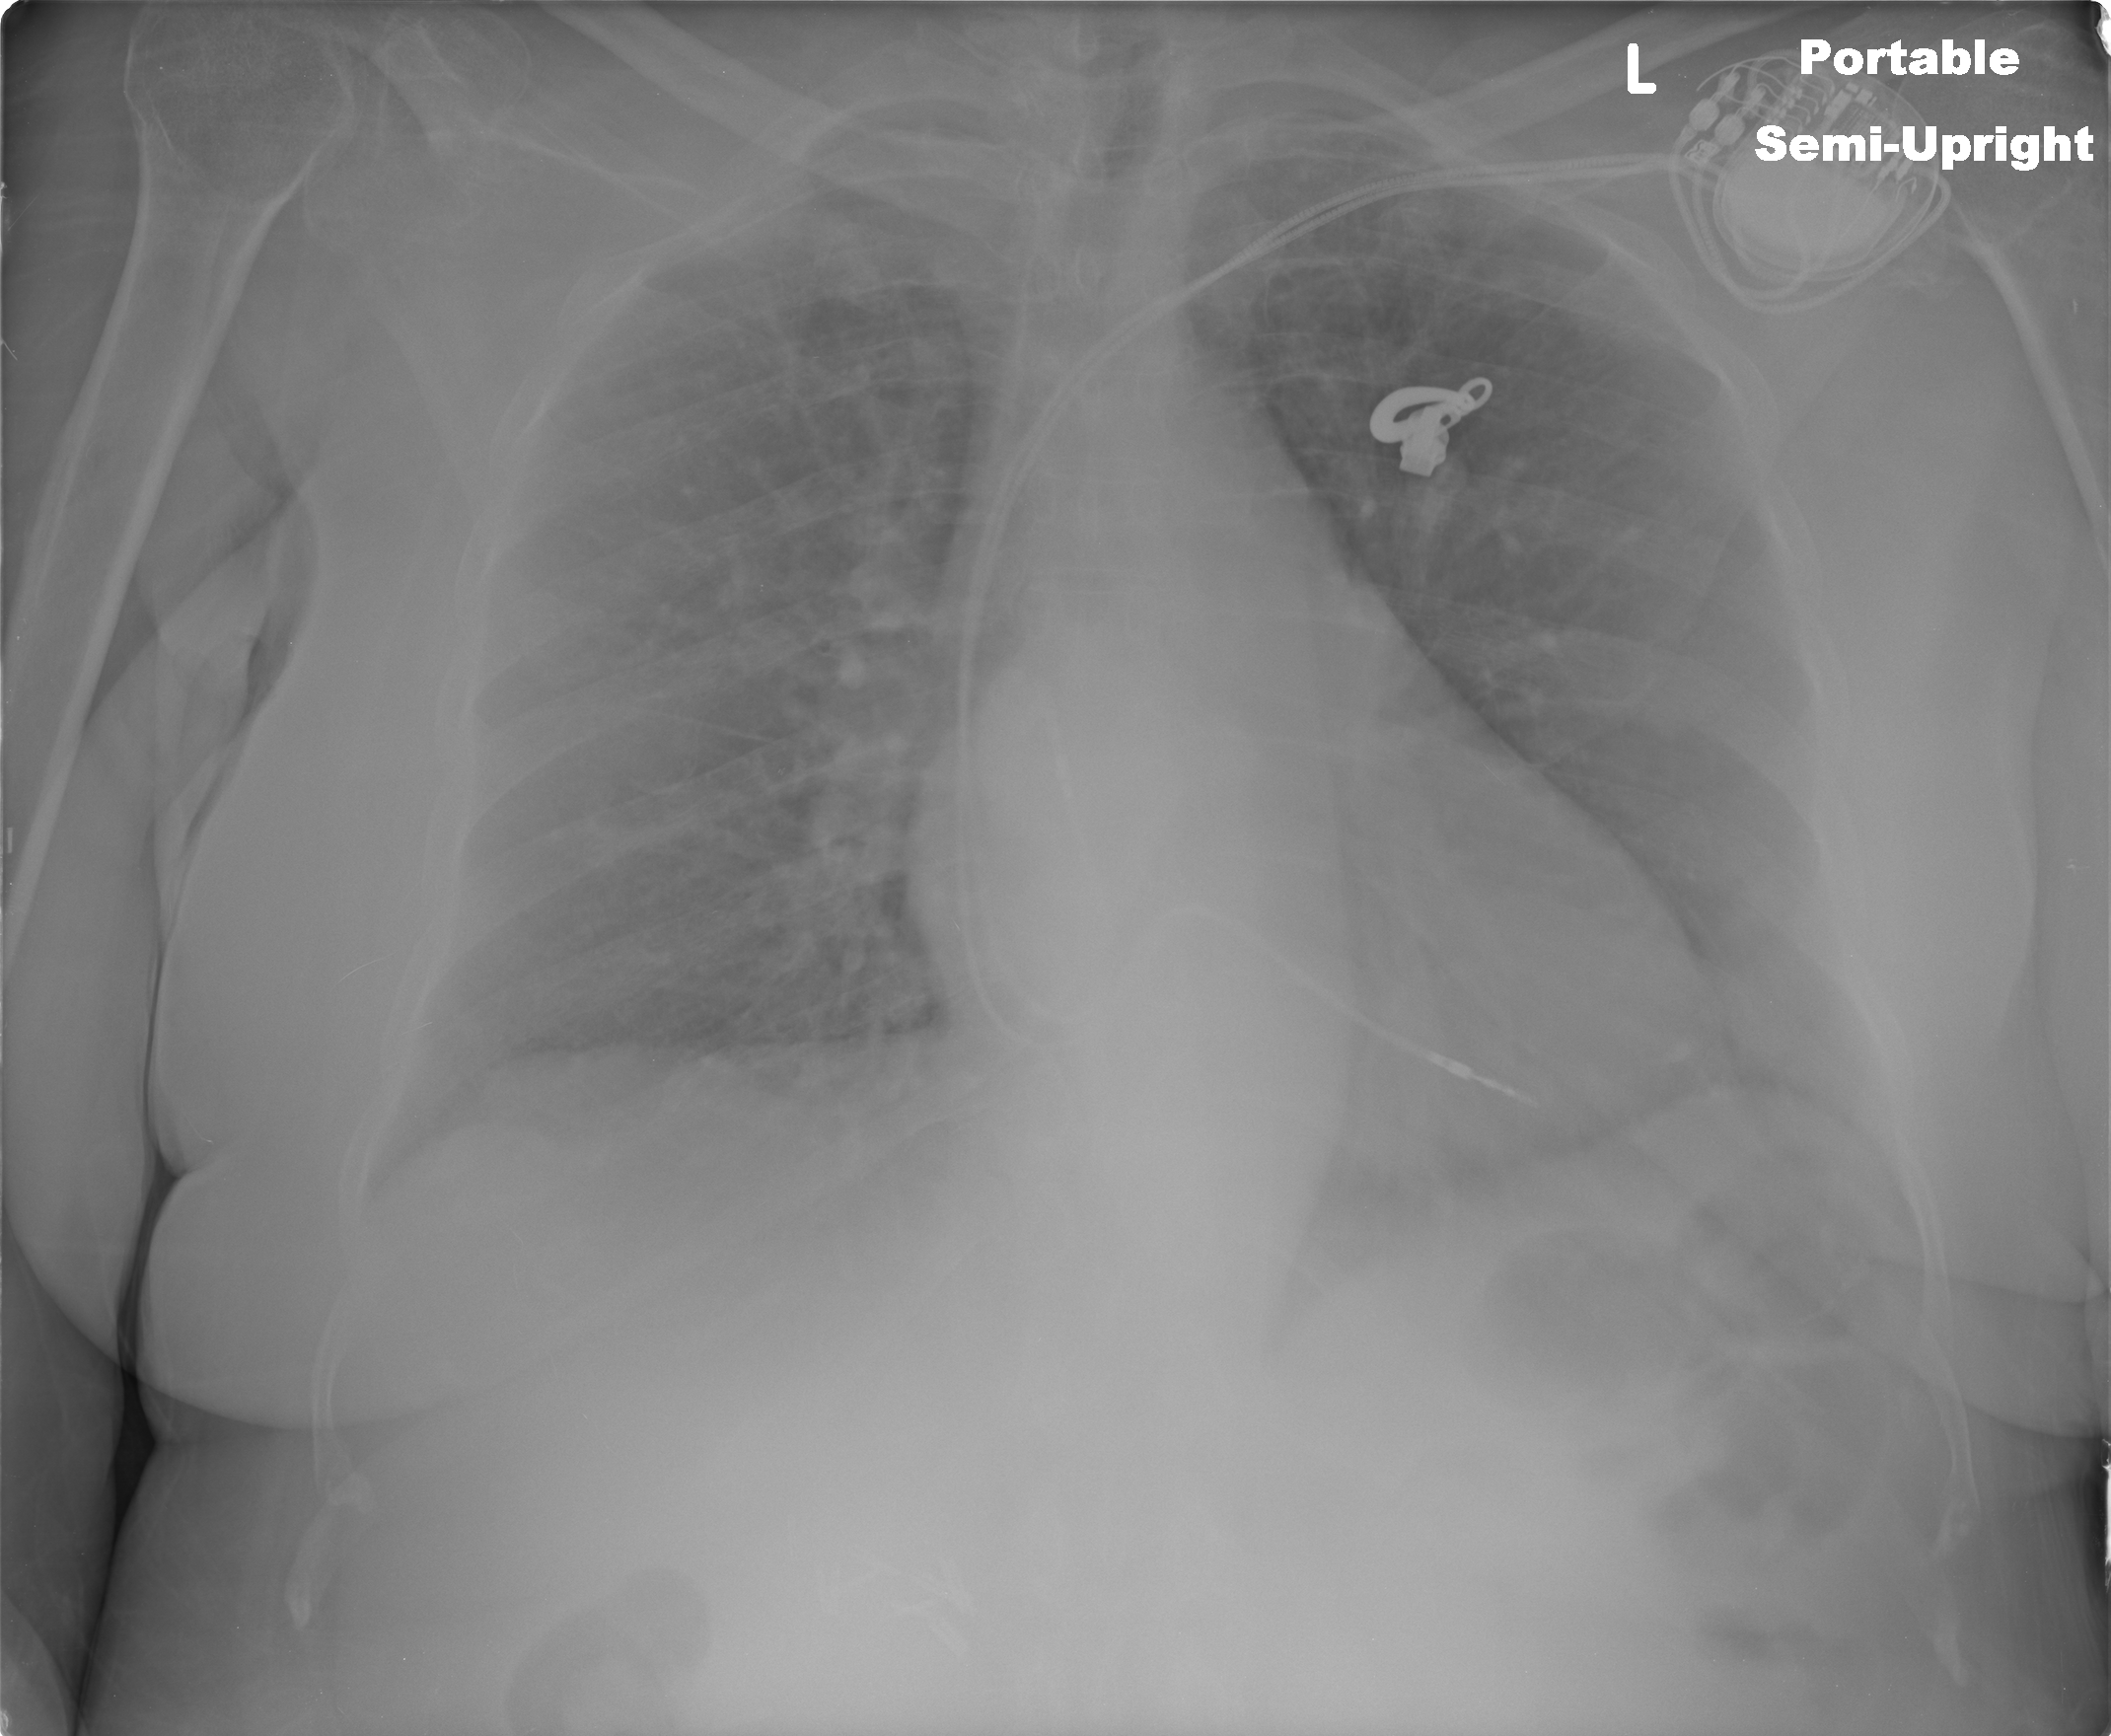
Chest X-ray (portable), AP projection. Female patient, age 77 years; imaged 5 days after the COVID-19 diagnosis.
Key findings recorded by the radiologist: no acute airspace changes seen in both lungs.